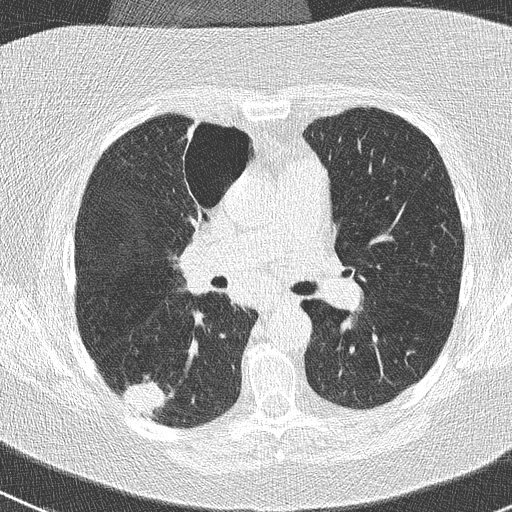
Axial slice from a low-dose chest CT screening exam, first (baseline) screen, lung window (W 1500 / L -600 HU), lung (sharp) reconstruction kernel (B50f), slice 110 of 261 in the series, 512 × 512 image matrix, field of view 310 × 310 mm. Female, age 74 years at enrolment. Former smoker at enrolment.
Lesion marked by an expert reader, bounding box <117,377,174,426> (left, top, right, bottom; pixels). The screening reader recorded 3 non-calcified nodules or masses ≥4 mm on this exam (right lower lobe, right upper lobe, left lower lobe); which of them this box marks is not recorded. Official screen result: positive, change unspecified: nodule(s) >= 4 mm or enlarging nodule(s), mass(es), or other non-specific abnormalities suspicious for lung cancer. Later outcome: lung cancer diagnosed 16 days after this screen — non-small cell carcinoma, right lower lobe, poorly differentiated (G3), stage IIIA (AJCC 6th edition), 28 mm at pathology.